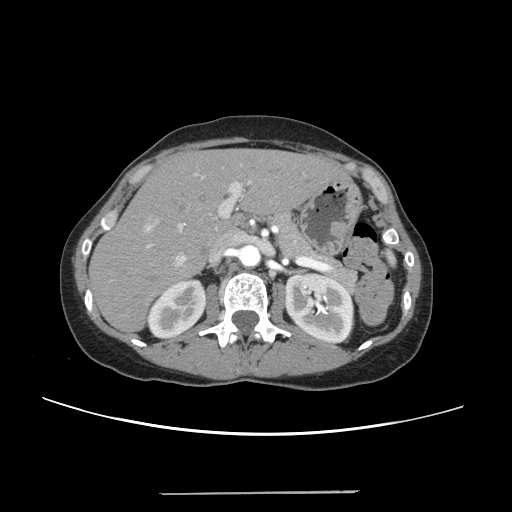
Contrast-enhanced abdominal CT, one axial slice; position 150 of 240 along the scan axis; 120 kVp; intravenous contrast given; soft-tissue window (W 400 / L 40 HU); 1.25 mm slice thickness; 512 × 512 image matrix, field of view 371 × 371 mm. Female patient, age 60 years. Case-level facts recorded for this patient, not image findings: diagnosis: colorectal cancer liver metastases, imaged before liver resection; multiple liver metastases: no; largest metastasis: 1.5 cm; disease in both lobes: no.
Structures marked on this image (manually delineated by an expert):
- liver: box from (x=91, y=150) to (x=344, y=330) px
- planned liver remnant (the part of the liver to remain after resection): (x=91, y=150)–(x=343, y=330)
- portal vein (with intrahepatic branches): (x=143, y=164)–(x=253, y=266)